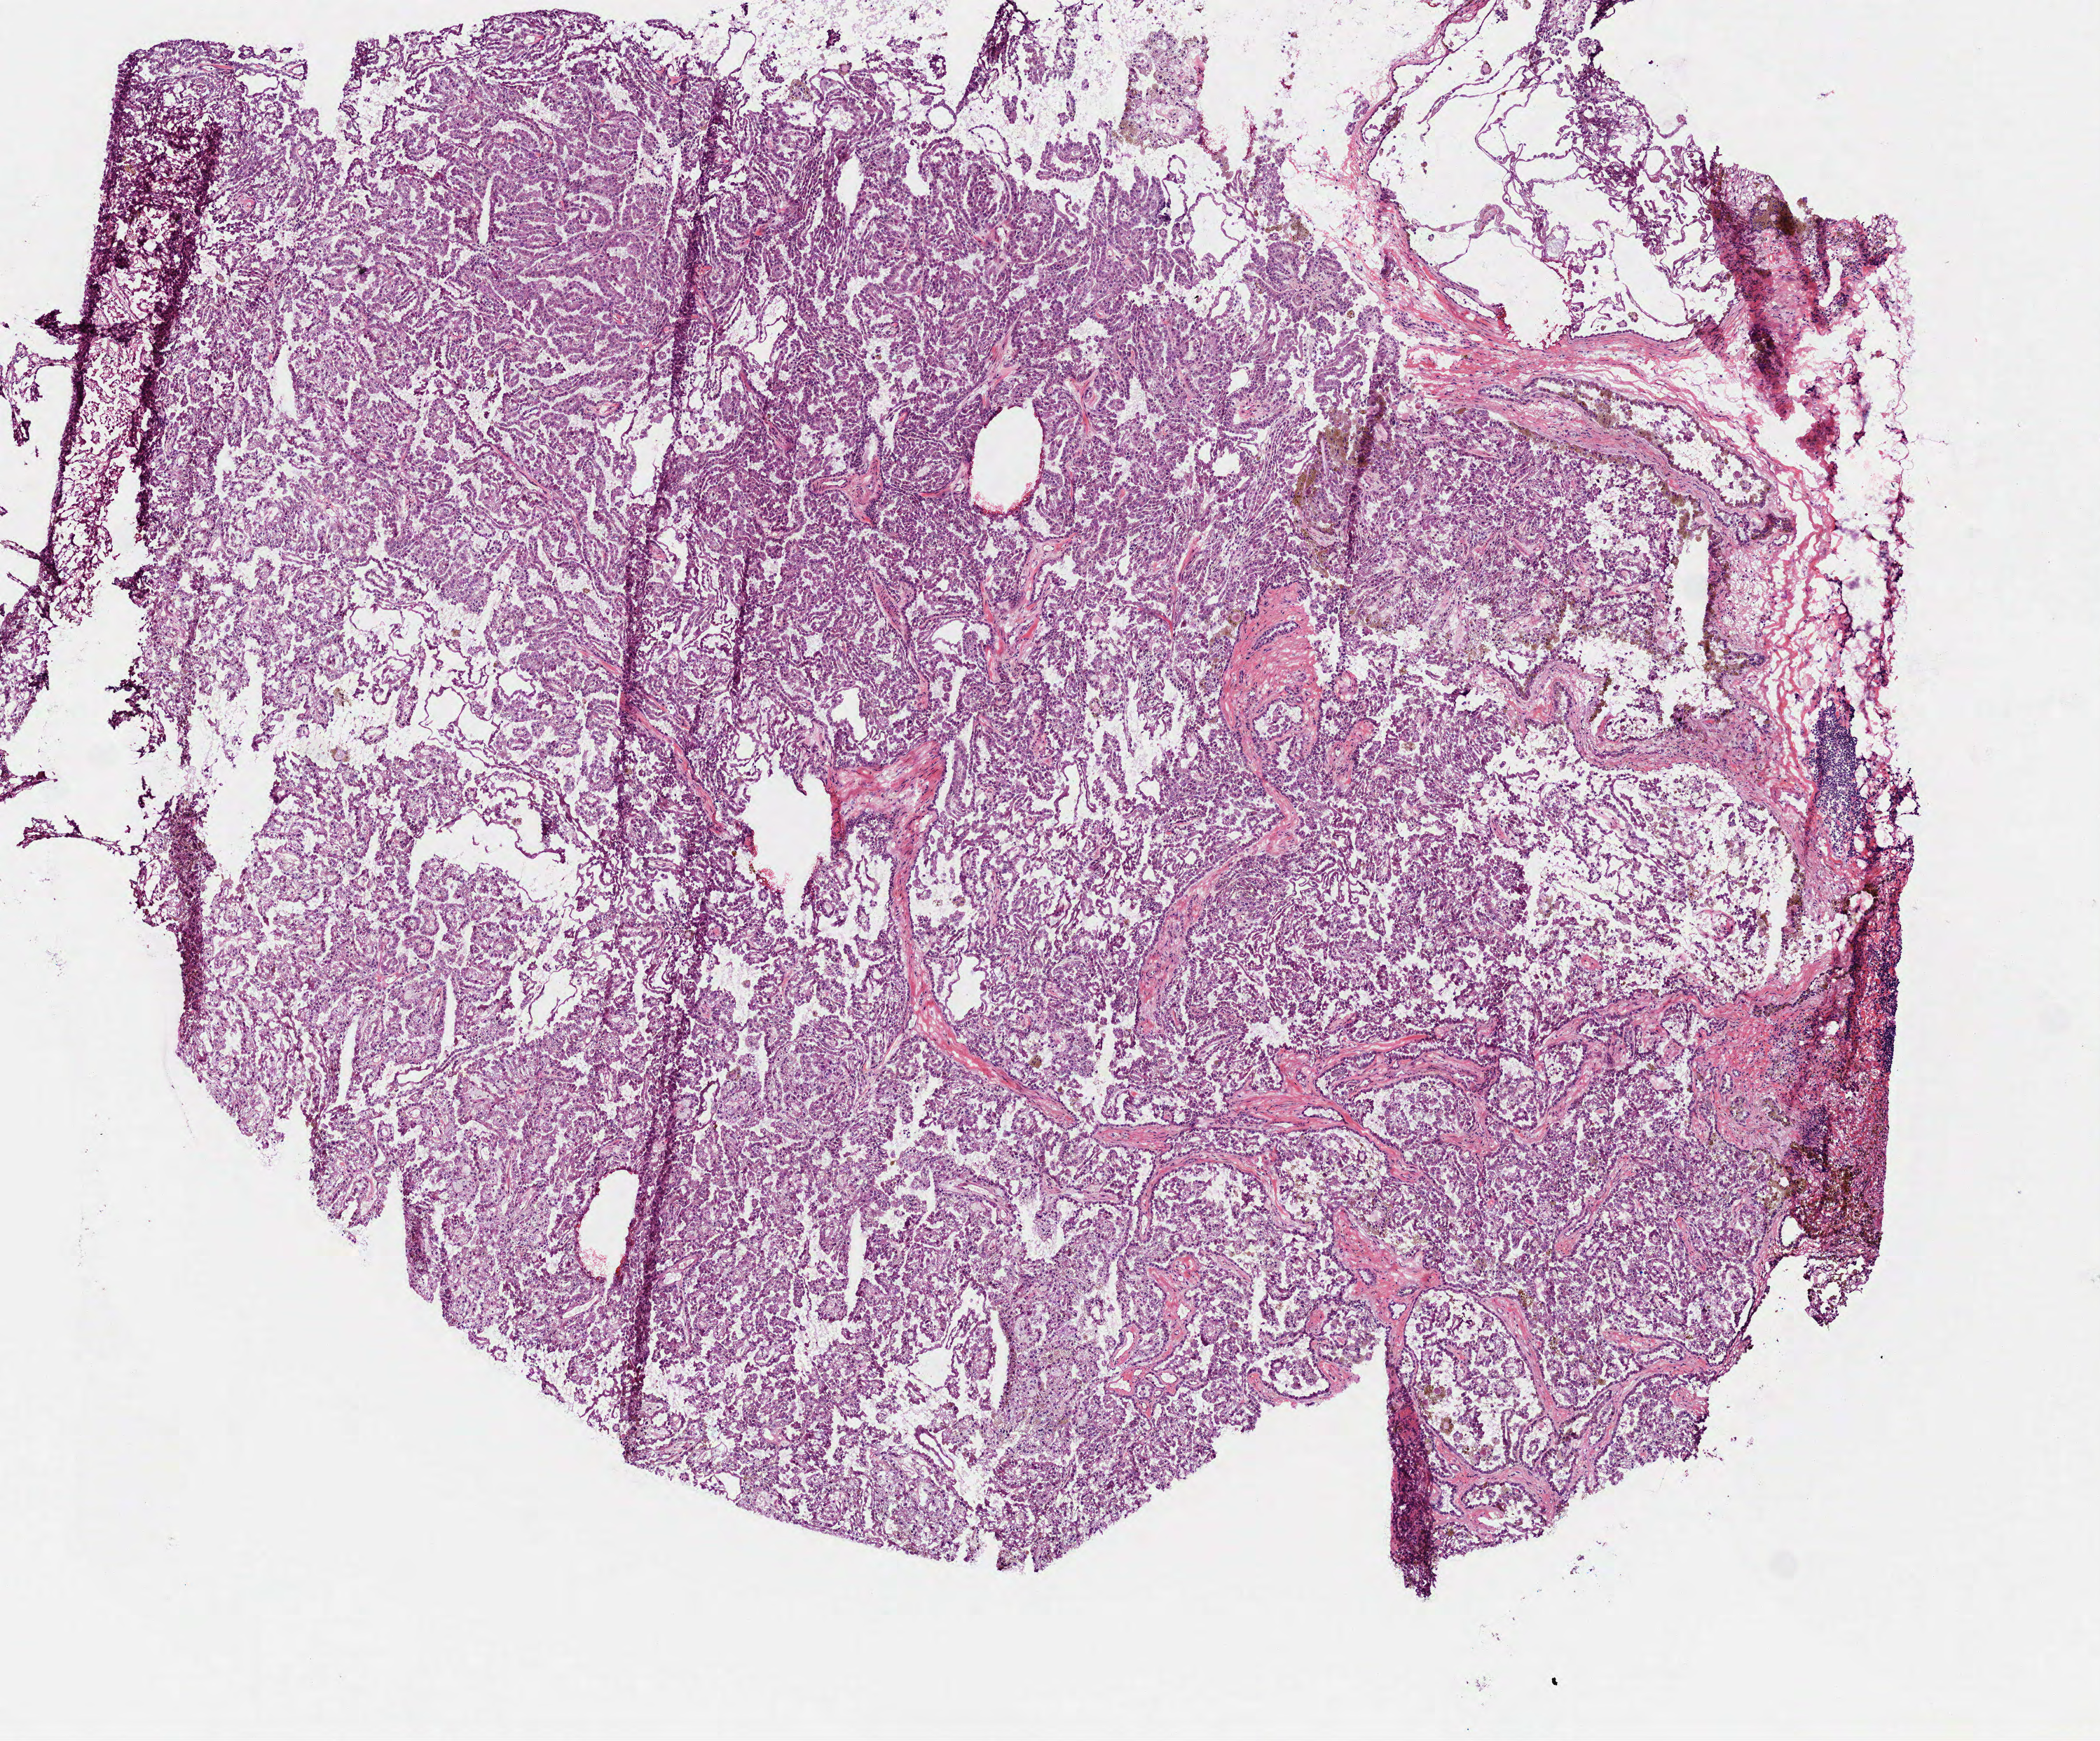
Hematoxylin and eosin (H&E) stained whole-slide image, whole scanned area (about 6.0 x 5.0 mm) shown as a low-resolution overview, frozen section from the bottom of the tissue portion, kidney, primary tumour sample. Female, age 71 years at initial diagnosis. Pathologist review of this section (percent, as recorded): tumour cells 95%, tumour nuclei 85%, normal cells 0%, stromal cells 5%, necrosis 0%.
- laterality: right
- histologic diagnosis: Papillary adenocarcinoma, NOS